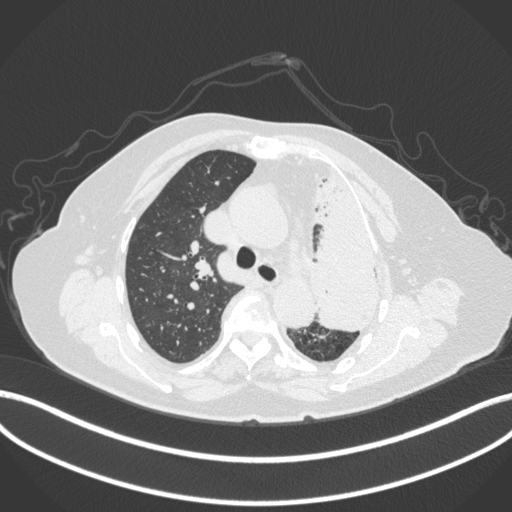
Chest CT, one axial slice; reconstruction kernel B31f; 120 kVp; lung window (W 1500 / L -600 HU); 1 mm slice thickness; 512 × 512 image matrix, field of view 400 × 400 mm. Patient: female, 75 years. From the clinical record (not read from this slice): clinical TNM (as recorded): T3 N3 M1.
Structures marked on this image (rectangle marked by the reading radiologist):
- lung tumour (recorded histology: adenocarcinoma): bounding box <305,155,391,339> (left, top, right, bottom; pixels)